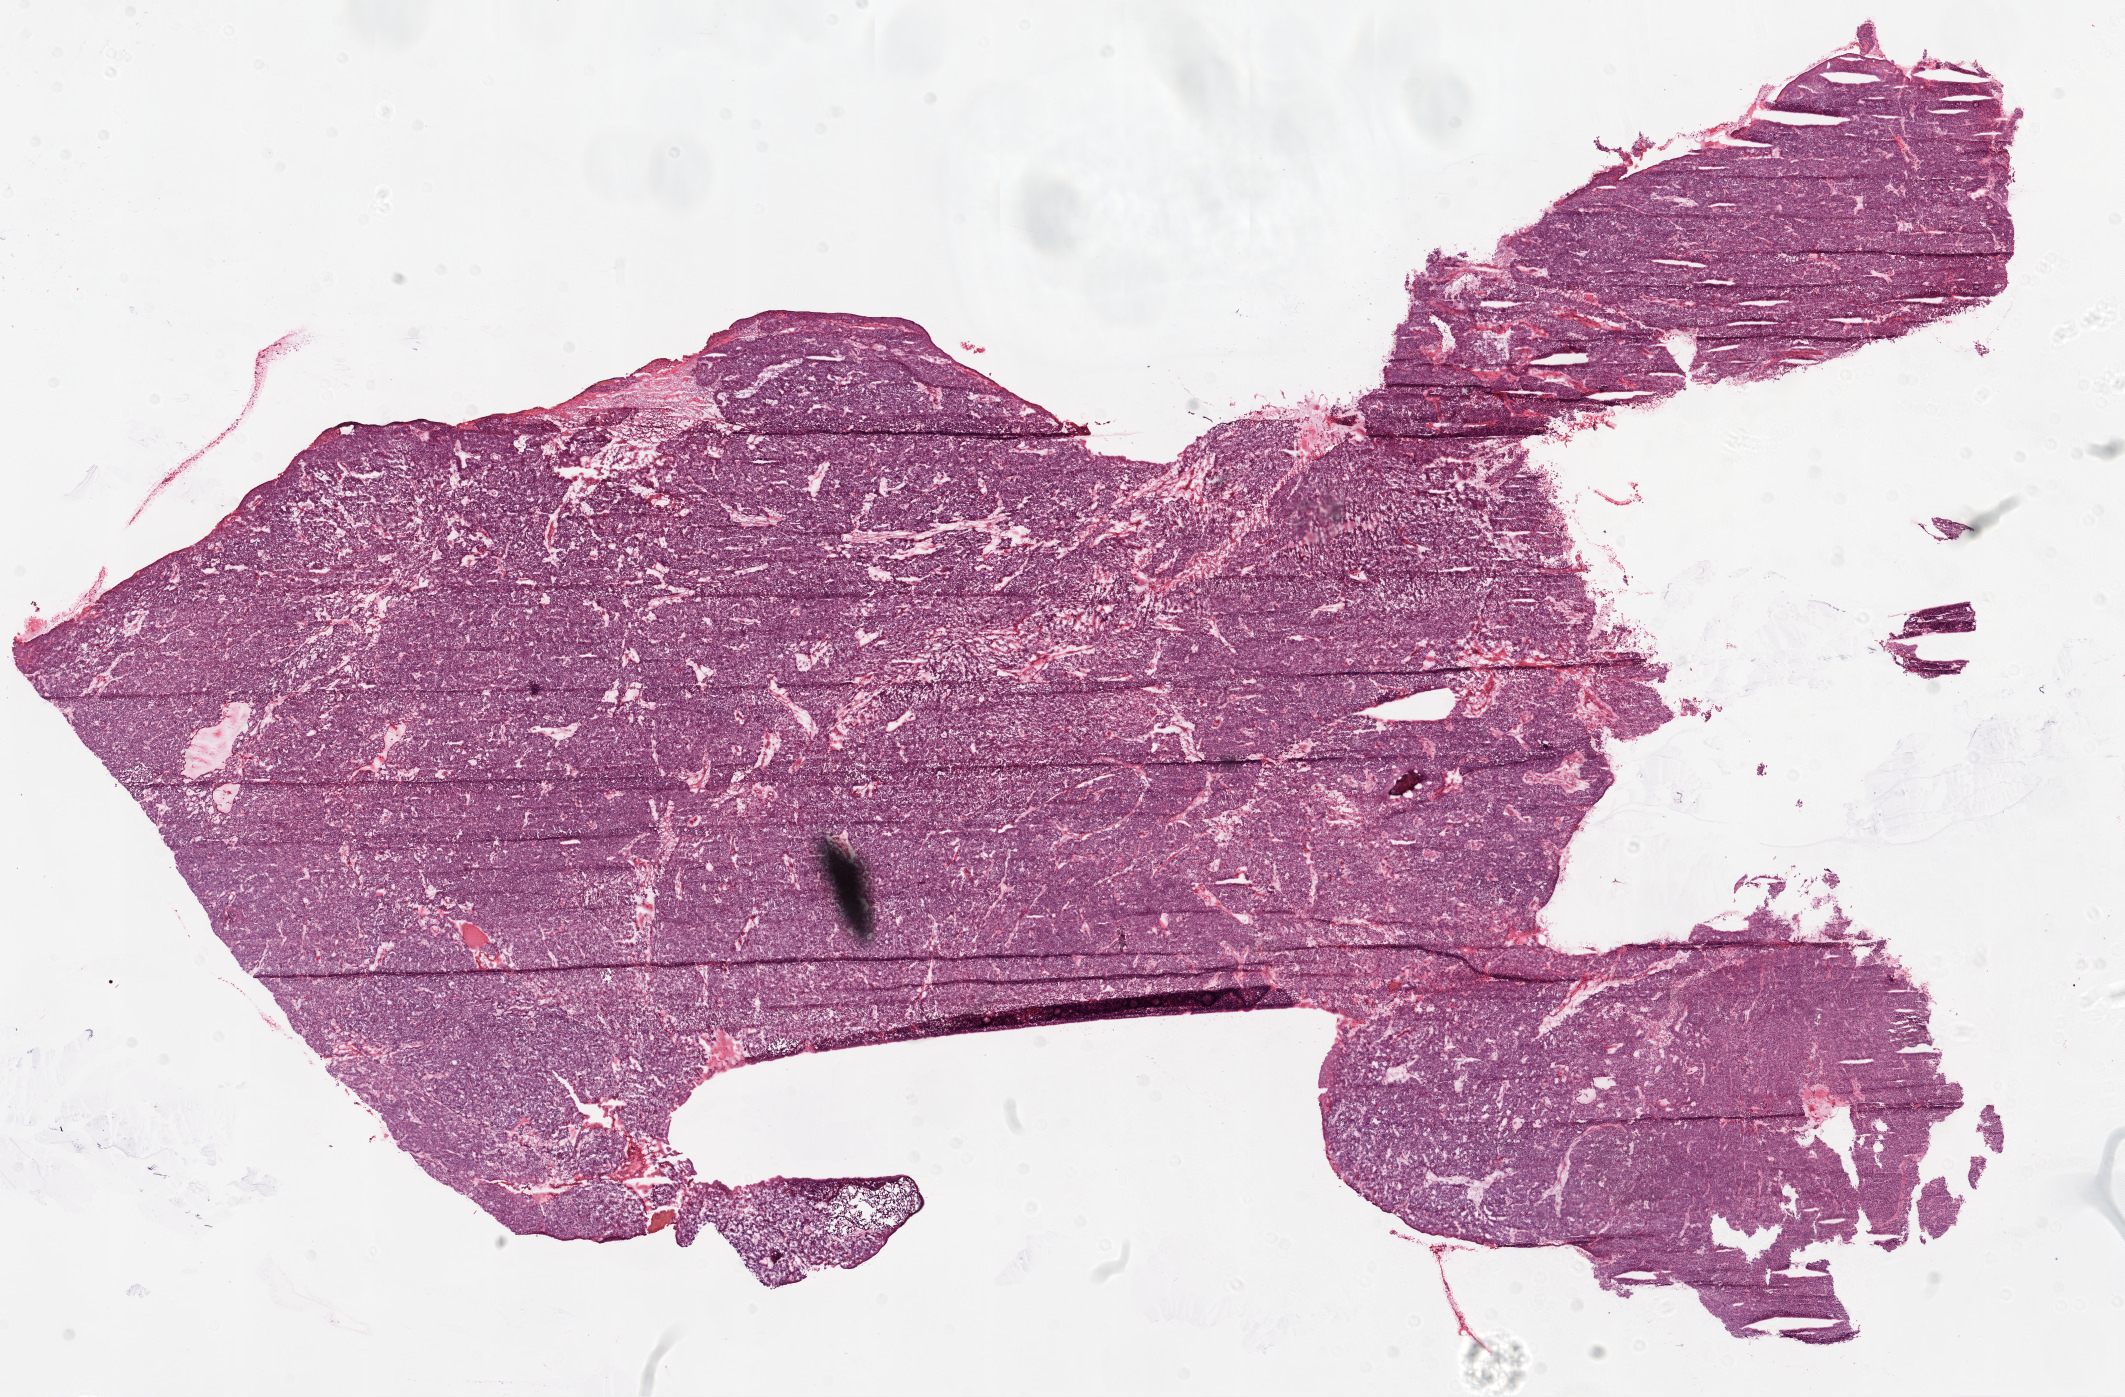
H&E-stained whole-slide image, a low-resolution overview of the entire scanned area, about 17.1 x 11.2 mm (acquisition: 20x scan). Frozen section from the top of the tissue portion. Sample: primary tumour, ovary. Patient: female, age at initial diagnosis 56 years. Histologic grade: G3 (poorly differentiated). Slide review estimates, as recorded: tumour cells 94%, tumour nuclei 95%, normal cells 0%, stromal cells 5%, necrosis 1%.
- FIGO stage: IIC
- laterality: bilateral
- histologic diagnosis: Serous cystadenocarcinoma, NOS